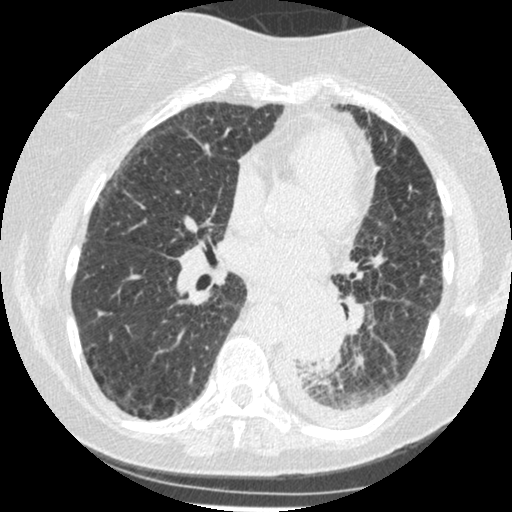
Axial slice from a low-dose chest CT screening exam, third screening round (two years after baseline), lung window (W 1500 / L -600 HU), 1.25 mm slice thickness, standard (soft-tissue) reconstruction kernel (STANDARD), slice 229 of 341 in the series, 512 × 512 image matrix. Female, age 60 years at enrolment.
Expert-annotated lung lesion, box from (x=275, y=304) to (x=343, y=375) px. The exam's reader record, not a measurement of the box and not confirmed to be the same lesion: non-calcified nodule or mass ≥4 mm, left lower lobe, 54 × 38 mm, smooth margins, soft tissue attenuation, pre-existing on the prior screen: yes; interval growth: yes. Official screen result: positive, other. Participant outcome: lung cancer diagnosed 15 days after this screen — small cell carcinoma, NOS, left lower lobe, undifferentiated (G4), stage IV (AJCC 6th edition), 69 mm at pathology.